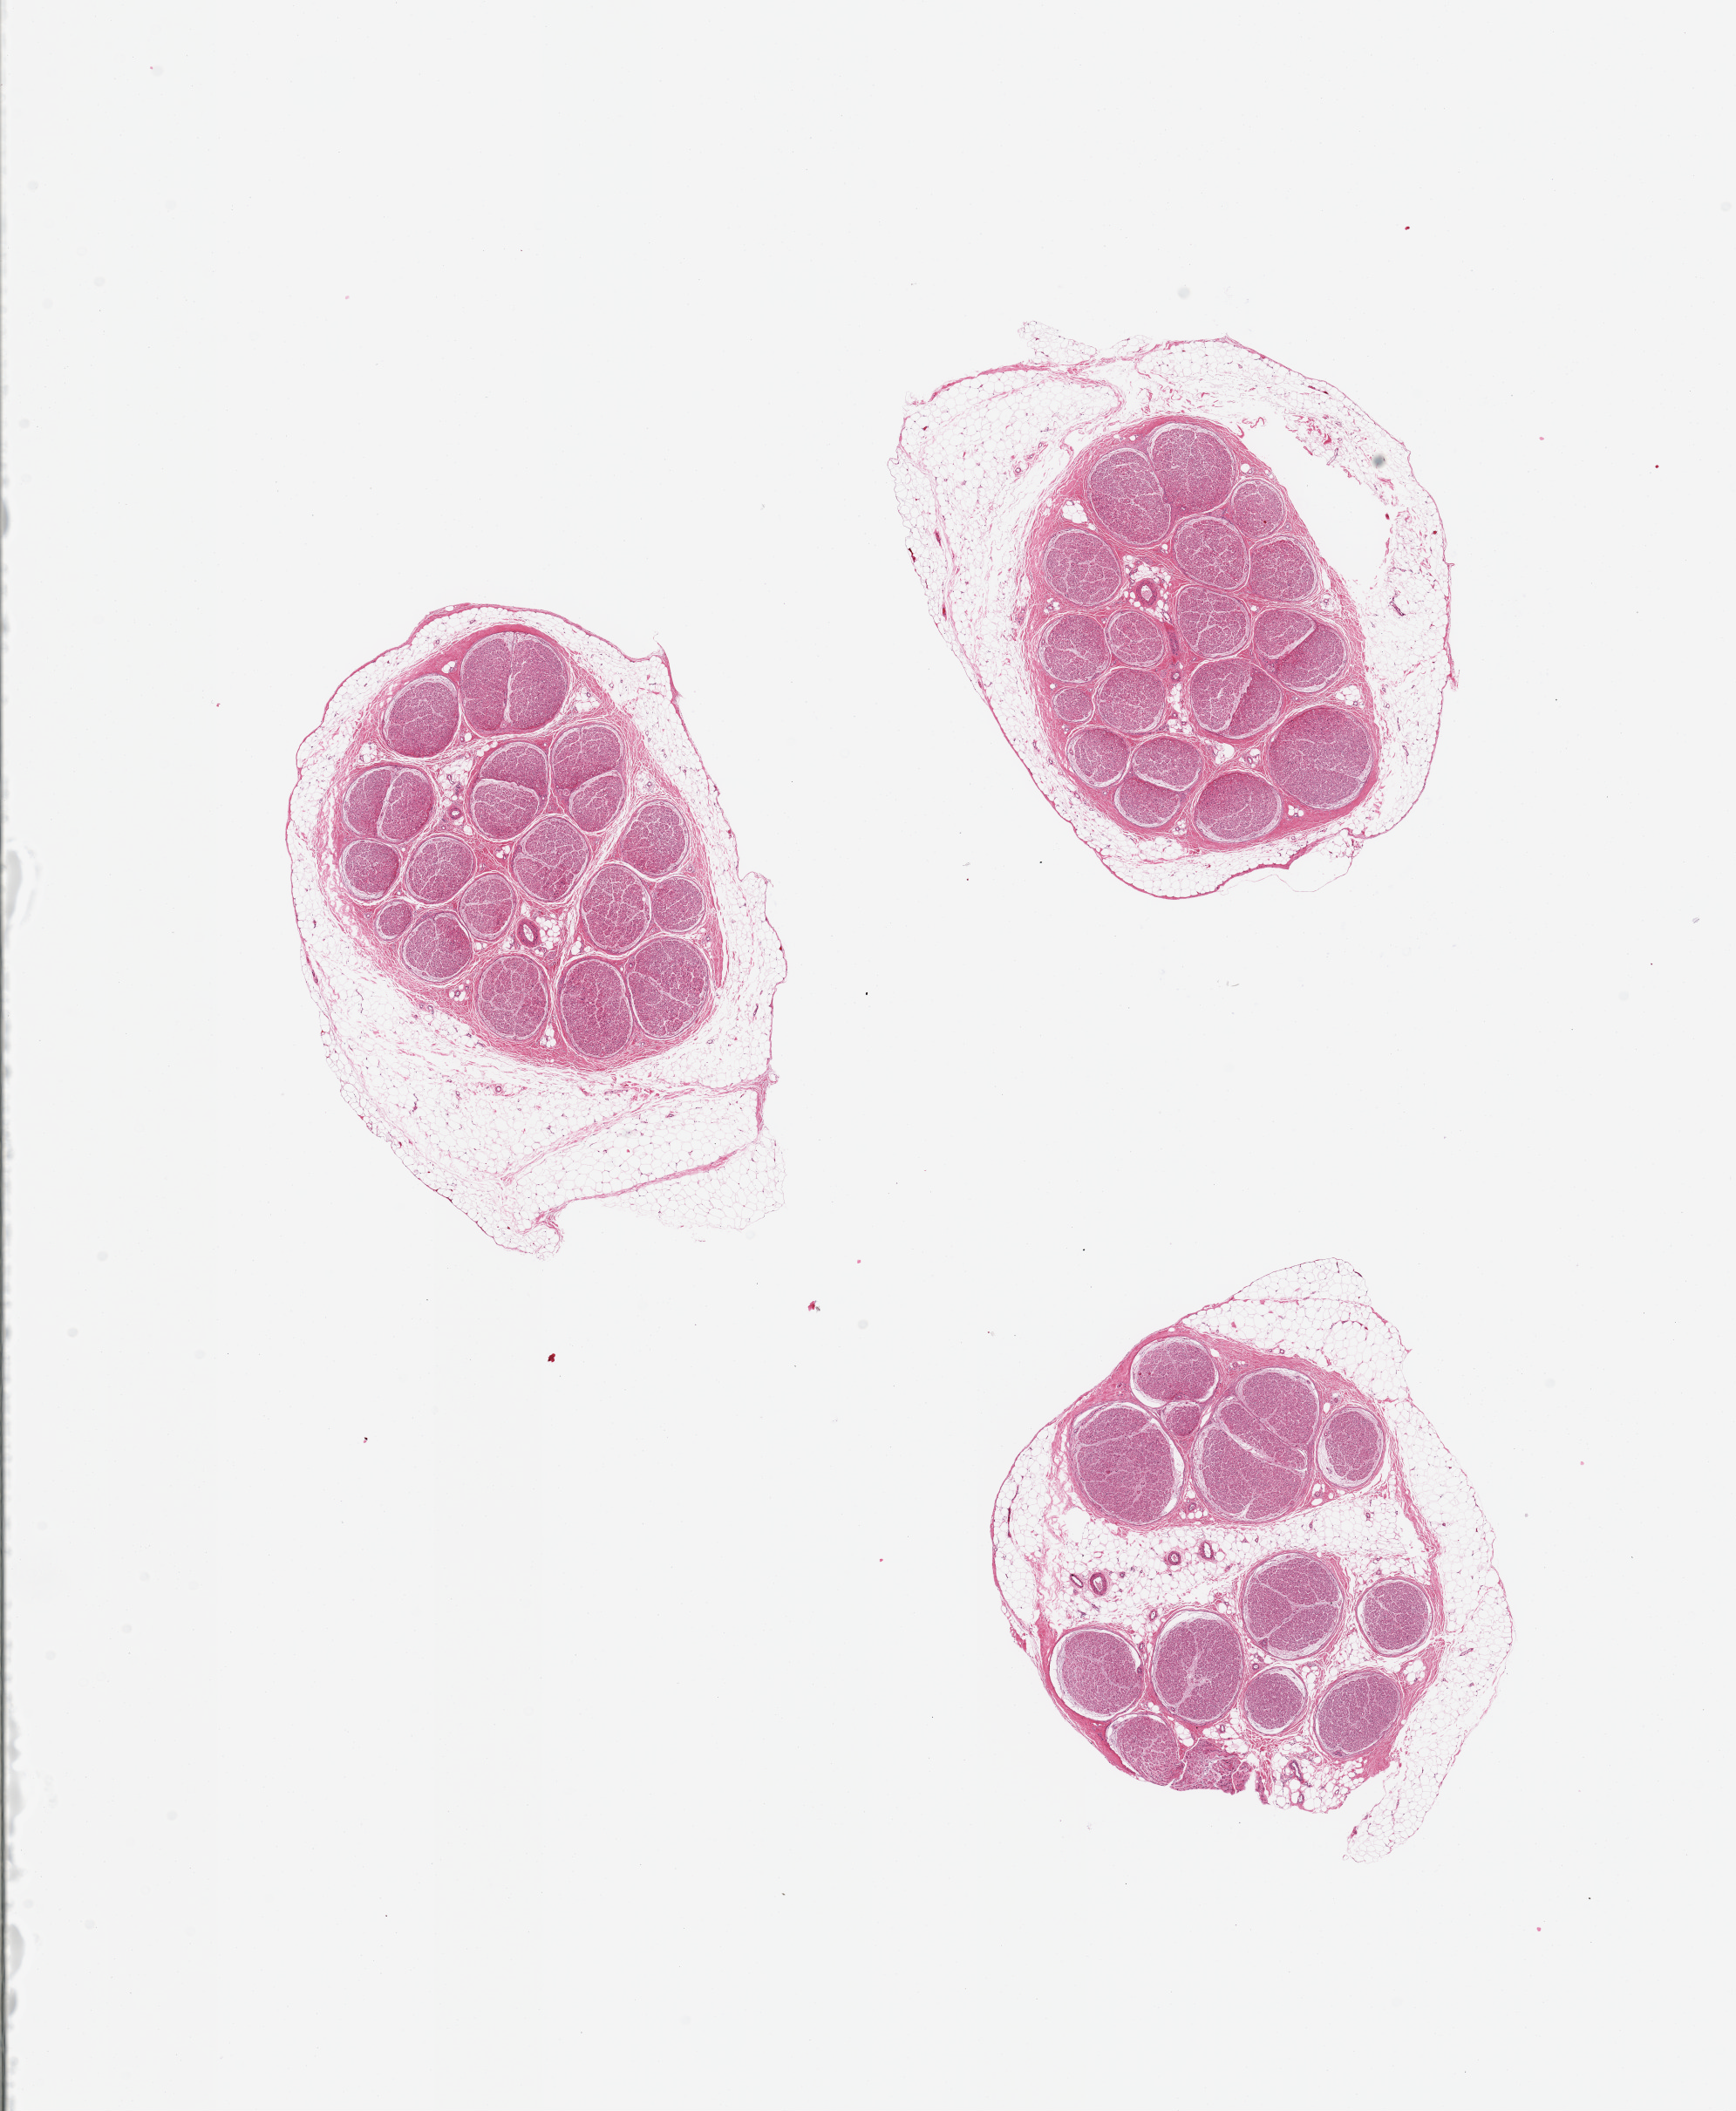
Whole-slide image, H&E stain, brightfield — whole scanned area (about 15.8 x 19.2 mm) shown as a low-resolution overview; PAXgene-fixed, paraffin-embedded tissue; target tissue: tibial nerve; tissue donor sample. Donor: male.
Reviewer comment on this tissue sample: 3 pieces; external fat up to 1.7mm; trace to 25% internal fat.